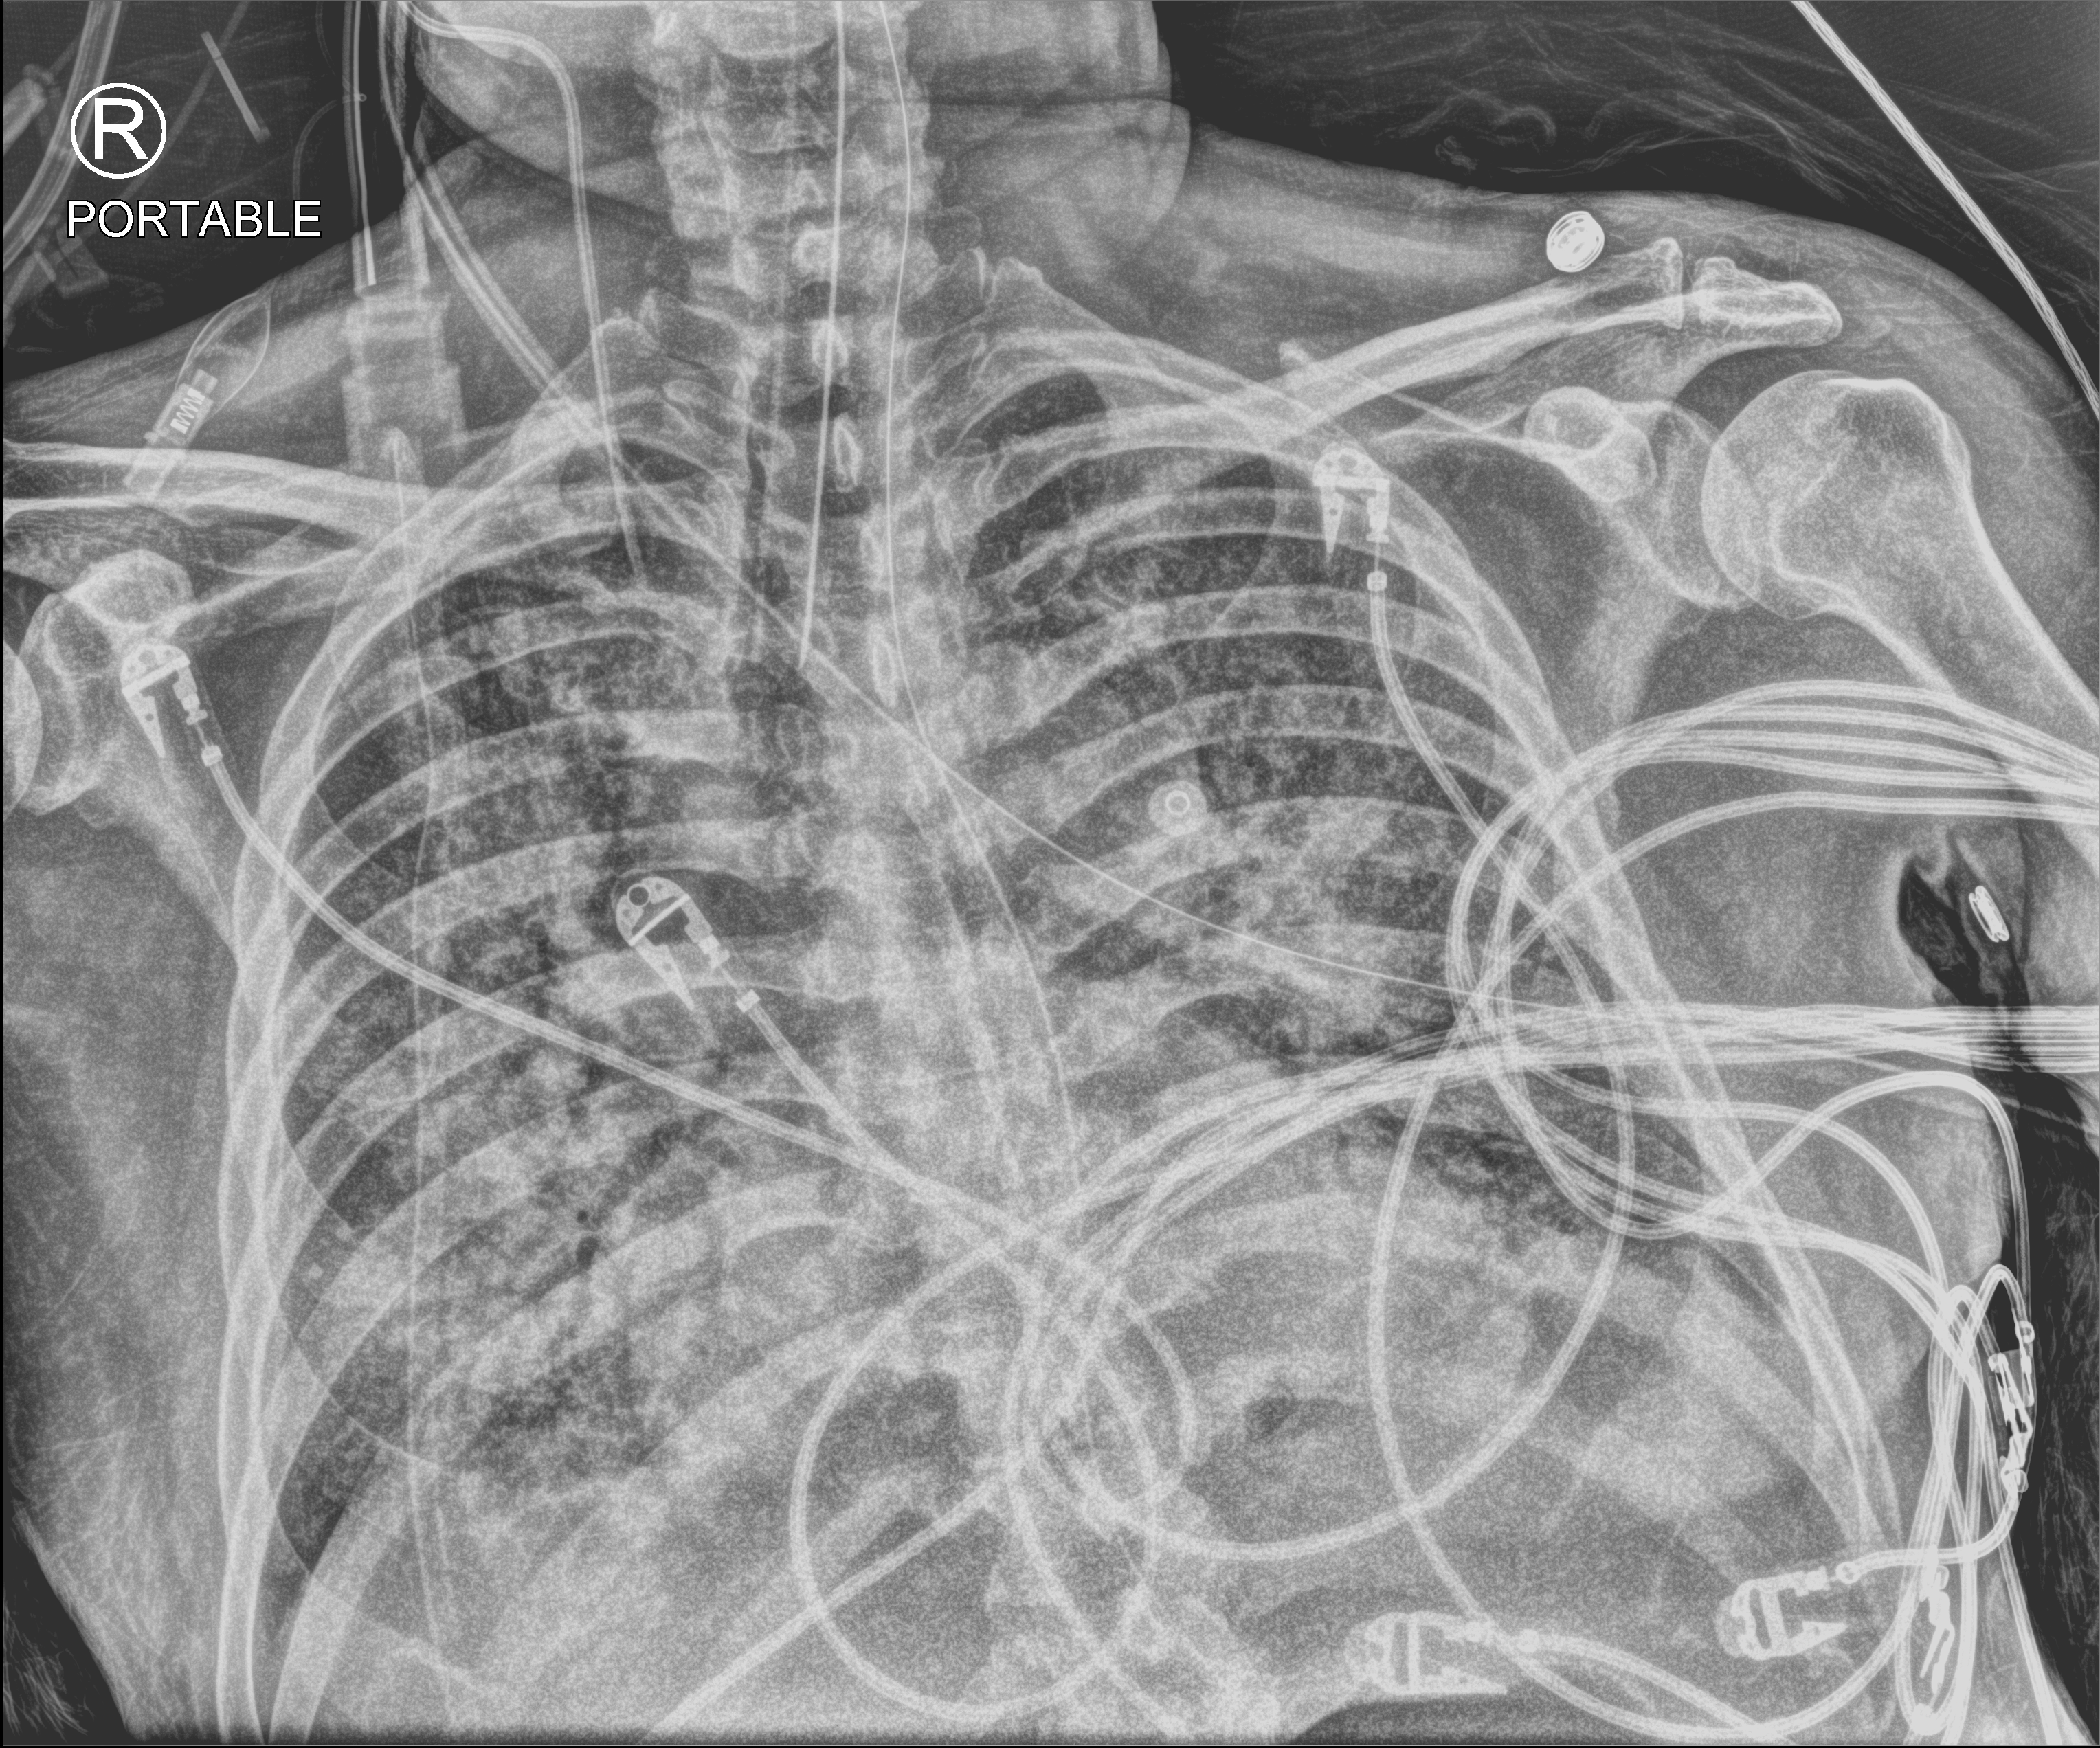
Chest X-ray (portable), anteroposterior (AP) projection. Male patient hospitalised with COVID-19, age 60–74 years.
Hospital-stay facts (about this admission, not read from this image; timing relative to this image not recorded): hypertension (admission record): yes.